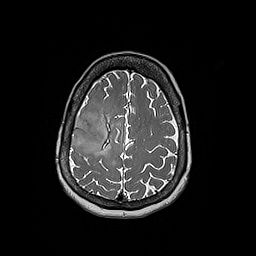
Brain MRI from a brain-tumour surgery series, one axial slice. 256 × 256 image matrix, field of view 250 × 250 mm. From the clinical record (not read from this slice): histopathology: Oligodendroglioma; WHO grade: 3; IDH mutation: yes.
Outlined on this slice (manually delineated by an expert):
- tumour: bounding box (x1, y1, x2, y2) in pixels: (71, 115, 107, 153)